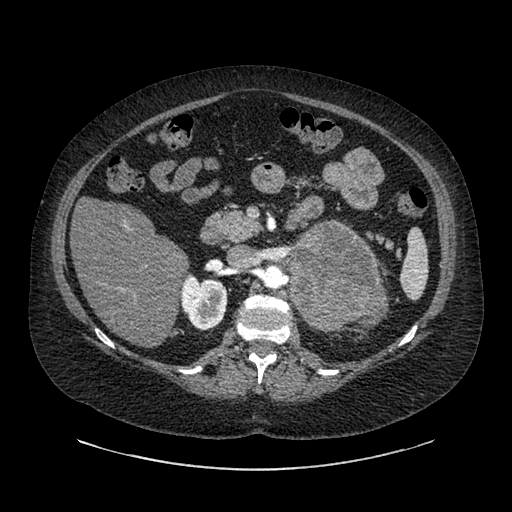
Contrast-enhanced abdominal CT, one axial slice; slice 541 of 769 in the series (ordered by position); reconstruction kernel SOFT; 120 kVp; intravenous contrast given; soft-tissue window (W 400 / L 40 HU); 0.62 mm slice thickness; 512 × 512 image matrix. Patient: female, 61 years. Case-level facts recorded for this patient, not image findings: diagnosis: adrenocortical carcinoma; tumour side: left adrenal; tumour size at pathology: 13 cm; Ki-67 index: 79 %; stage (as recorded): 2.
Outlined on this slice (semi-automatic segmentation, software-assisted and operator-edited):
- mass: bounding box (x1, y1, x2, y2) in pixels: (288, 225, 377, 329)